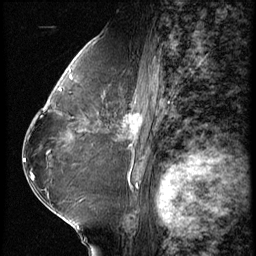
Breast MRI (dynamic contrast-enhanced), one sagittal slice. Position 34 of 62 along the scan axis. 3 images stored at this slice position (order not interpretable as contrast timing). 1.5 T. TE 4.2 ms, TR 9 ms. 2.5 mm slice thickness. 256 × 256 image matrix, field of view 180 × 180 mm. Female patient, age 65 years. Case-level facts recorded for this patient, not image findings: setting: breast cancer imaged before/during neoadjuvant chemotherapy; receptor status: HR-positive, HER2-negative.
Annotated regions visible in this slice (semi-automatic segmentation, software-assisted and operator-edited):
- analysis volume of interest (the breast-tissue region the enhancement analysis was run in; not a lesion): bounding box (x1, y1, x2, y2) in pixels: (104, 104, 154, 161)
- tumour enhancement mask (voxels above the 140 % enhancement threshold inside the analysis volume of interest): (125, 113, 143, 148)